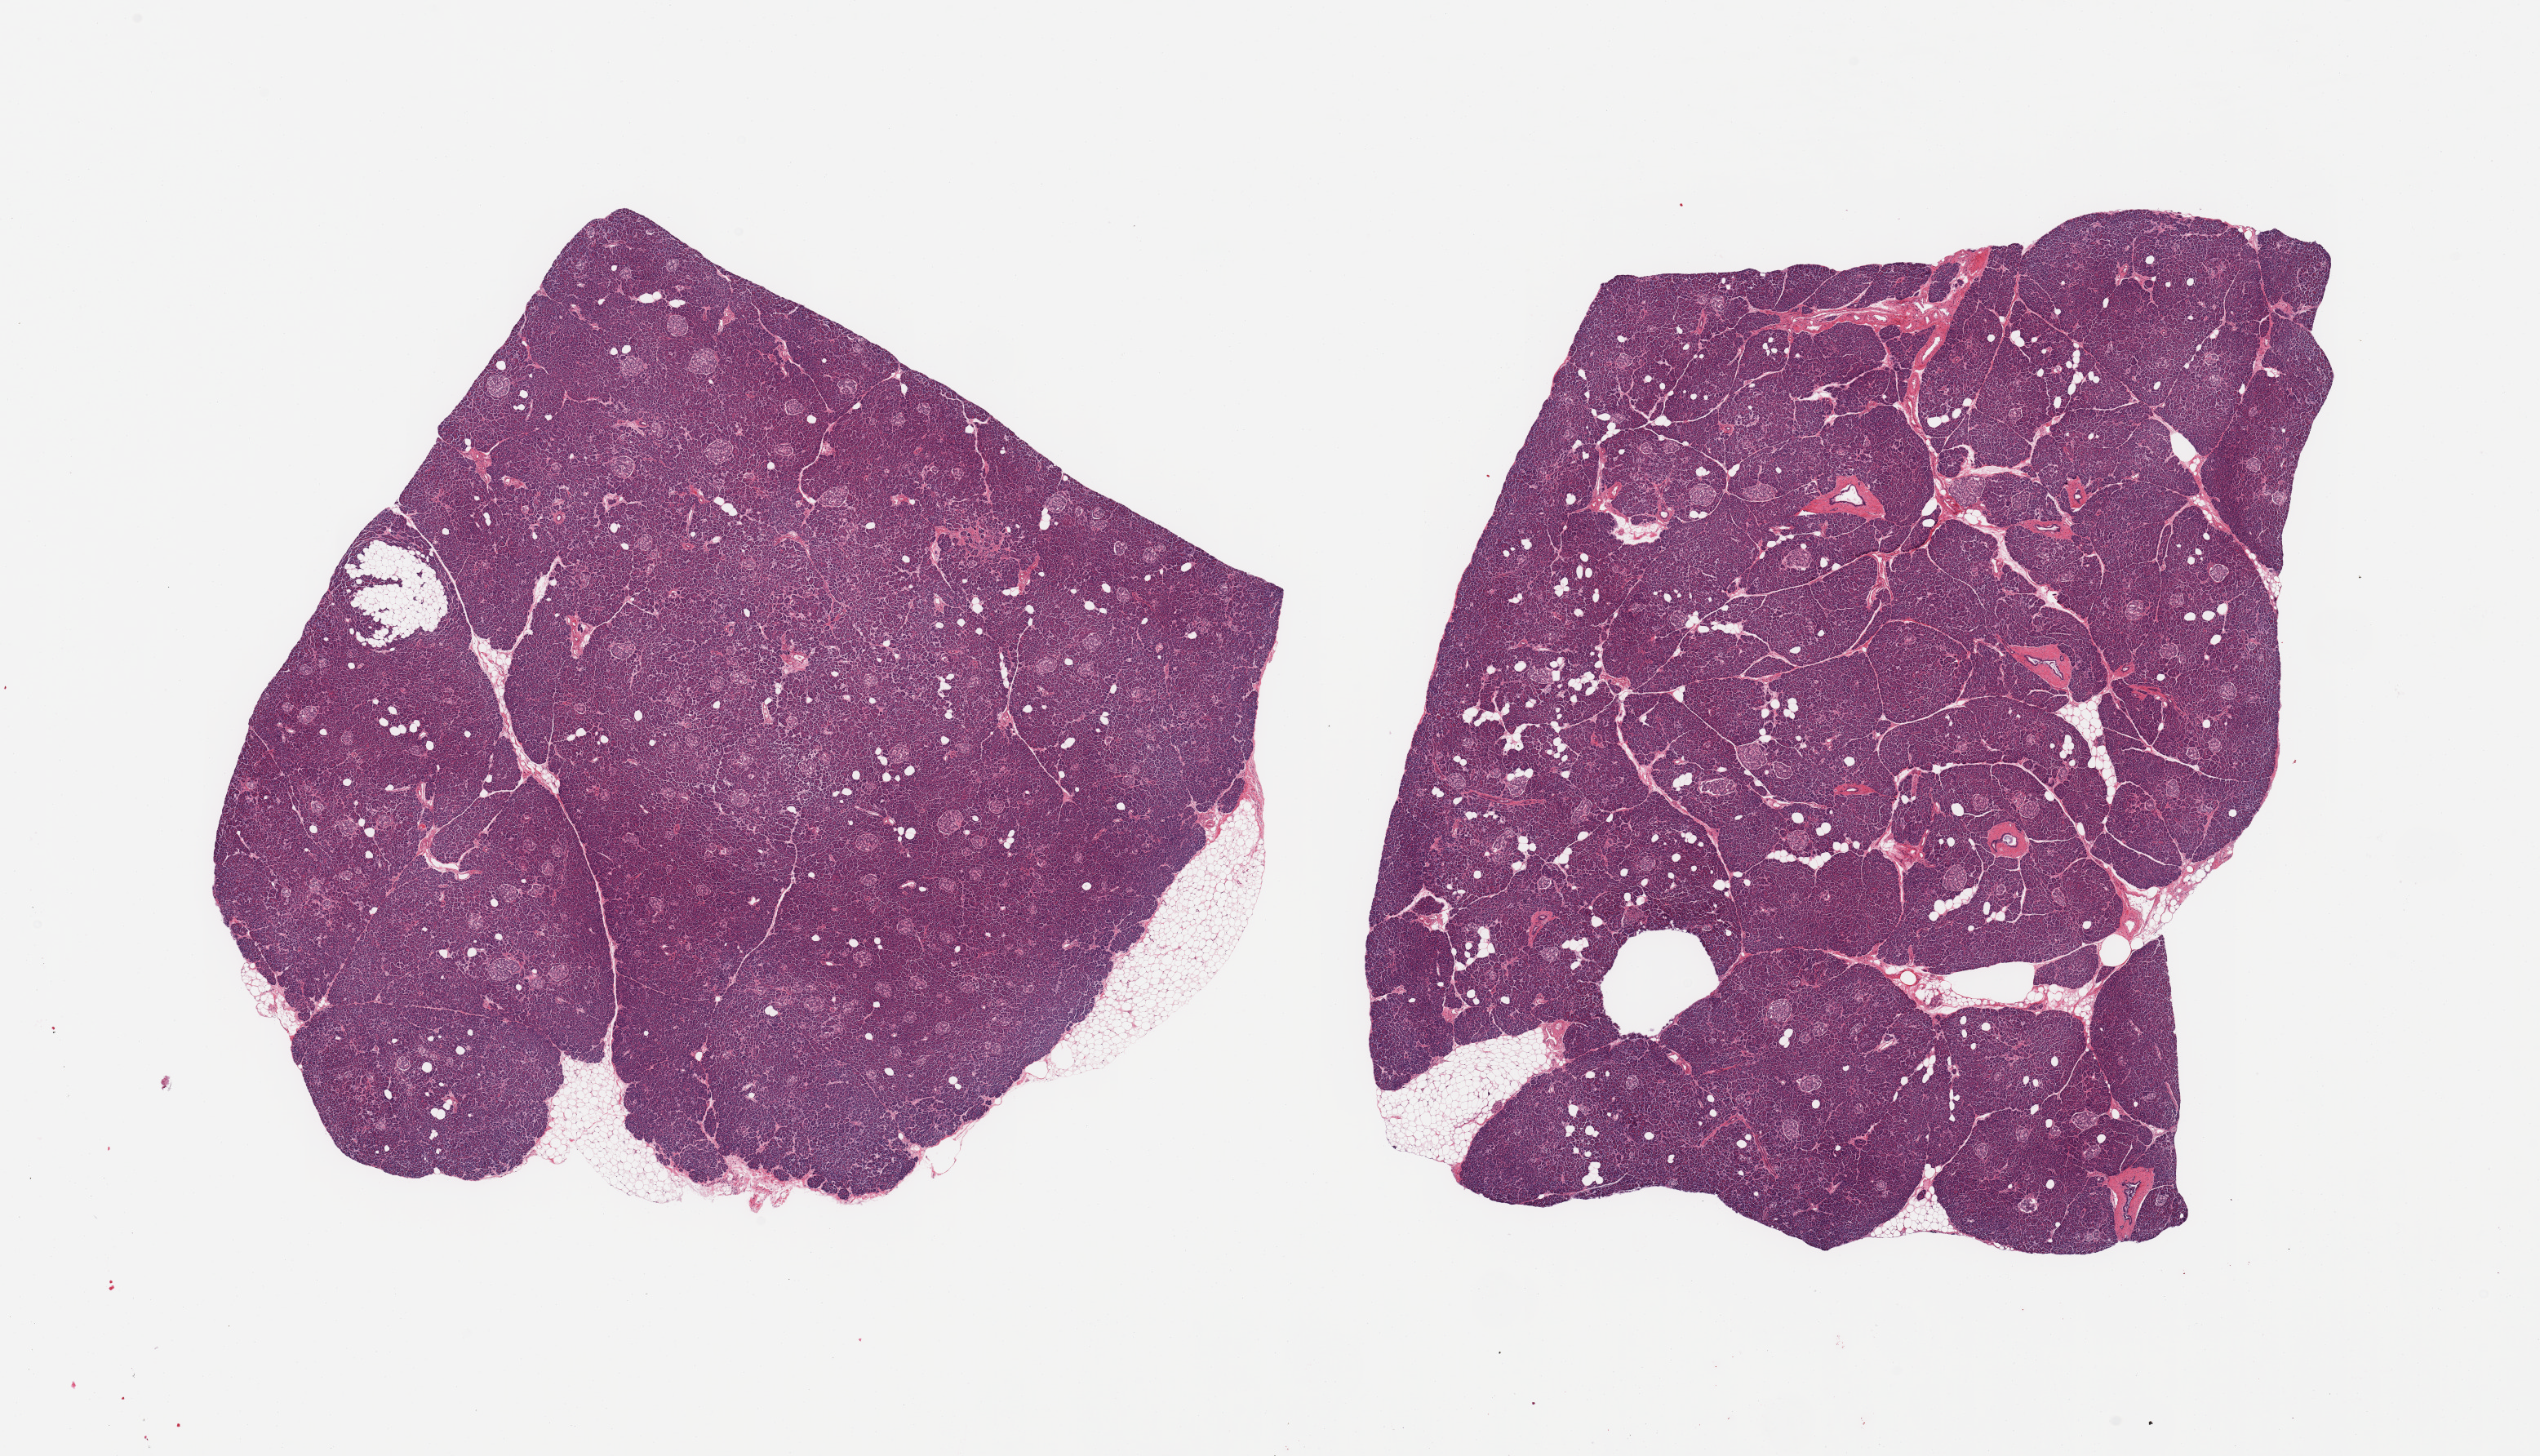
Digitized haematoxylin and eosin-stained section, shown as a low-resolution overview of the whole scanned area (about 24.6 x 14.1 mm, slide scanned at 20x). PAXgene-fixed paraffin-embedded (PFPE) section. Target tissue: pancreas. Tissue donor sample. Donor sex: female.
- pathologist's review note for this sample: 2 pieces; well preserved; 5% internal fat